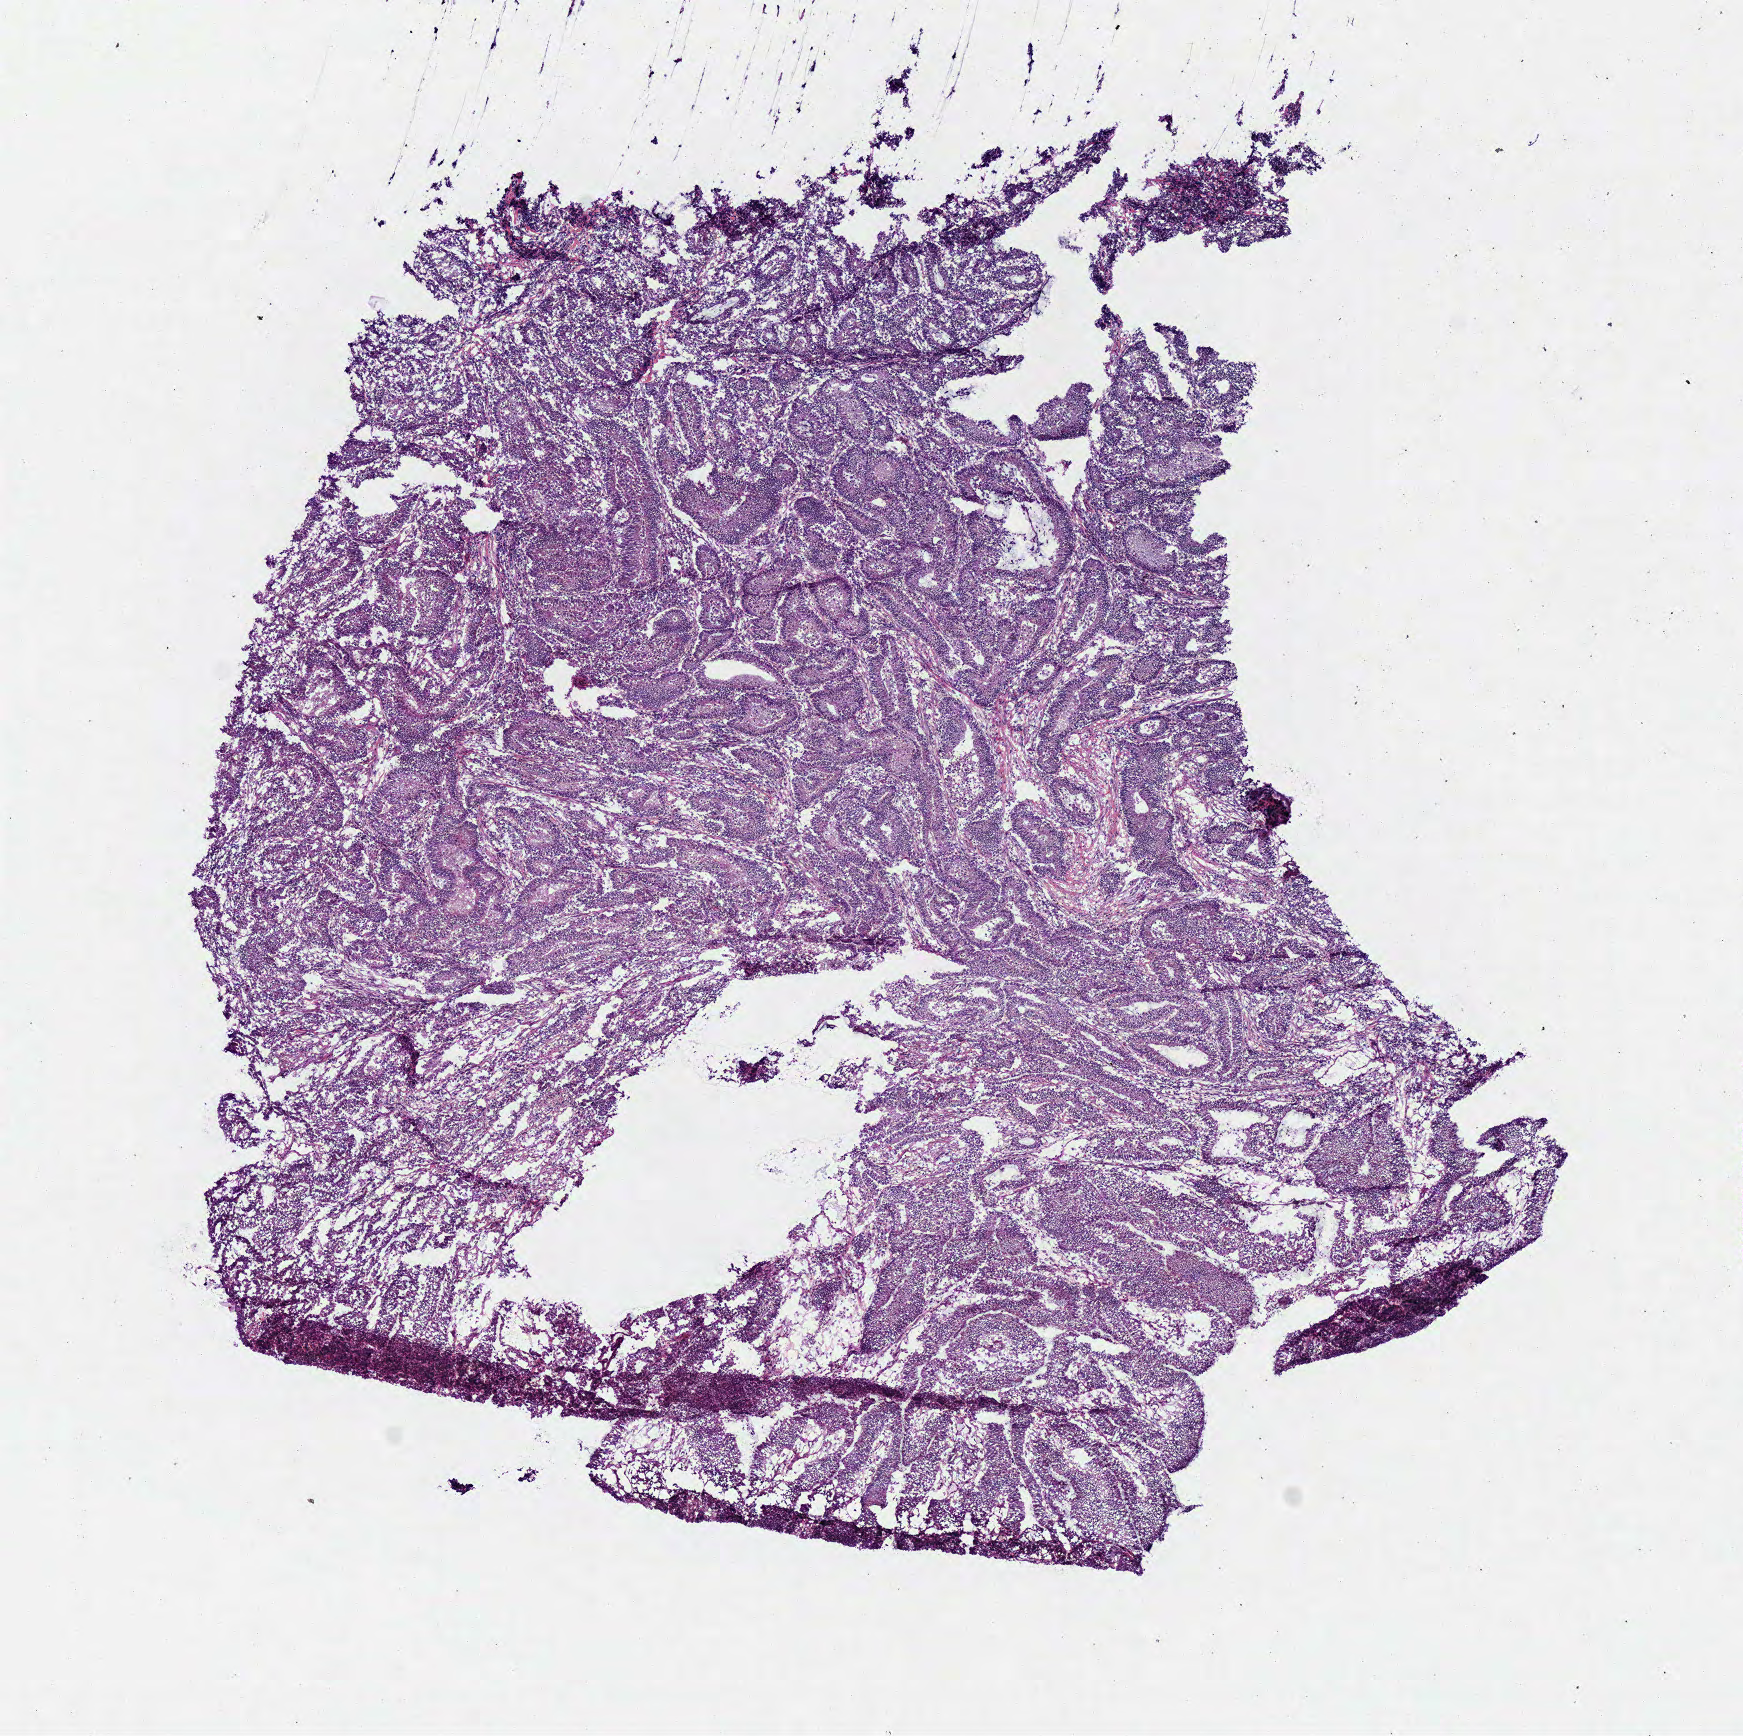
Digitized Hematoxylin and eosin (H&E) stained tissue section (whole slide) — a low-resolution overview of the entire scanned area, about 6.9 x 6.8 mm, frozen section, colon, primary tumour sample. Male patient; age at initial diagnosis 53 years. Composition of this section per pathologist review: tumour cells 99%, tumour nuclei 80%, normal cells 0%, stromal cells 0%, necrosis 1%. Infiltration values recorded for this section: lymphocyte infiltration 10%, monocyte infiltration 0%, neutrophil infiltration 5%.
AJCC pathologic stage: I (7th edition). Histologic diagnosis: Adenocarcinoma, NOS. Lymph nodes positive (case pathology): 0 of 15 examined.